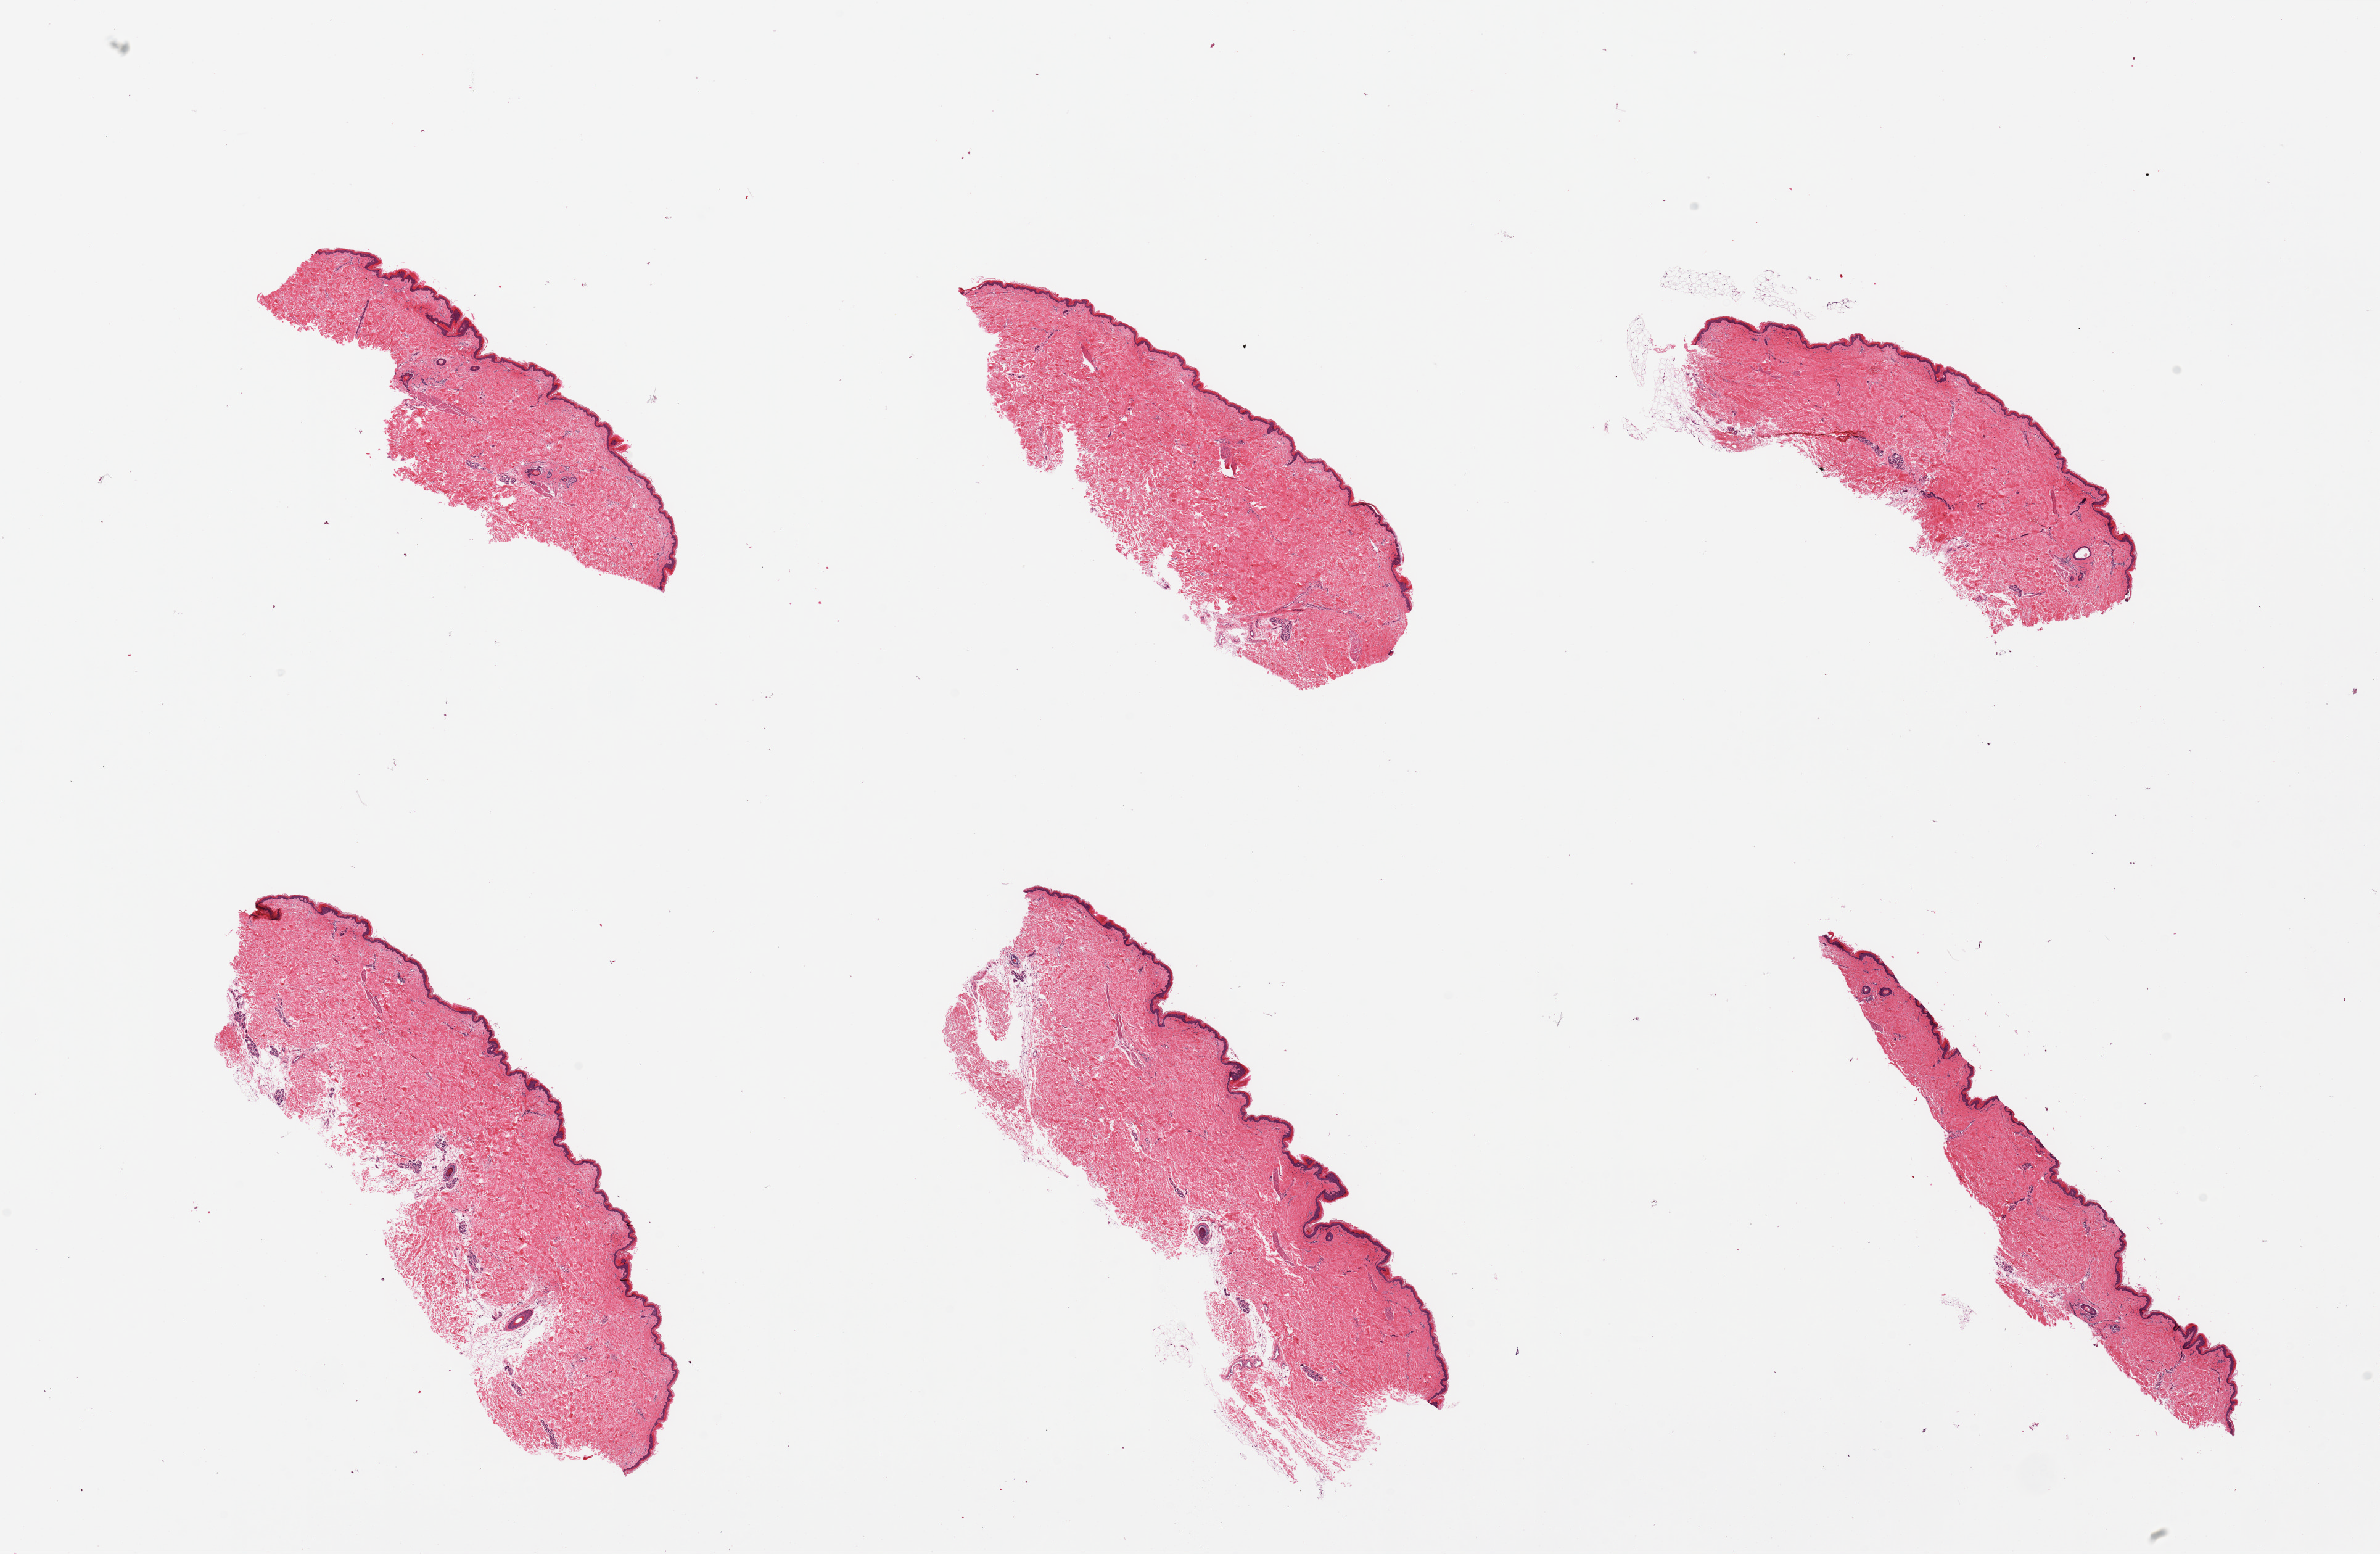
Whole-slide image, hematoxylin and eosin (H&E) stain, a low-resolution overview of the entire scanned area, about 30.5 x 19.9 mm. PAXgene-fixed, paraffin-embedded tissue. Target tissue: skin of lower leg. Donor tissue sample. Female donor.
* pathologist's review note for this sample: 6 pieces, well trimmed